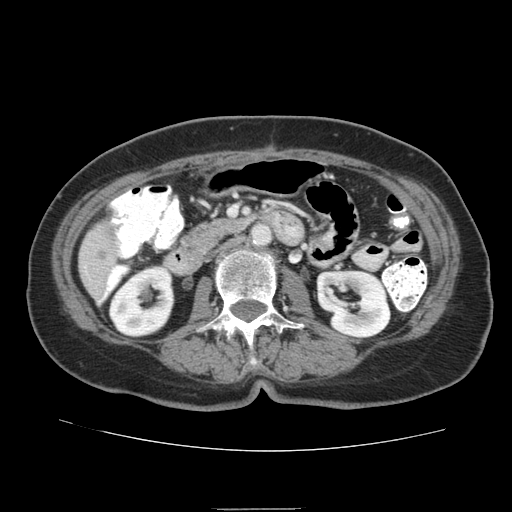
Contrast-enhanced abdominal CT (liver protocol), one axial slice. 140 kVp. Soft-tissue window (W 400 / L 40 HU). 2.5 mm slice thickness. 512 × 512 image matrix. Case-level facts recorded for this patient, not image findings: diagnosis: hepatocellular carcinoma (patient treated with transarterial chemoembolisation; whether this scan precedes or follows treatment is not stated here); TNM stage (as recorded): Stage-IVA; Child-Pugh class: B; tumour differentiation: moderately differentiated.
Structures marked on this image (semi-automatically segmented with operator editing):
- liver parenchyma outside the tumour (the mass and vessels are separate outlines, so this box may not span the whole liver): bounding box [x1, y1, x2, y2] px = [78, 218, 118, 305]
- liver vessels: [103, 287, 110, 299]